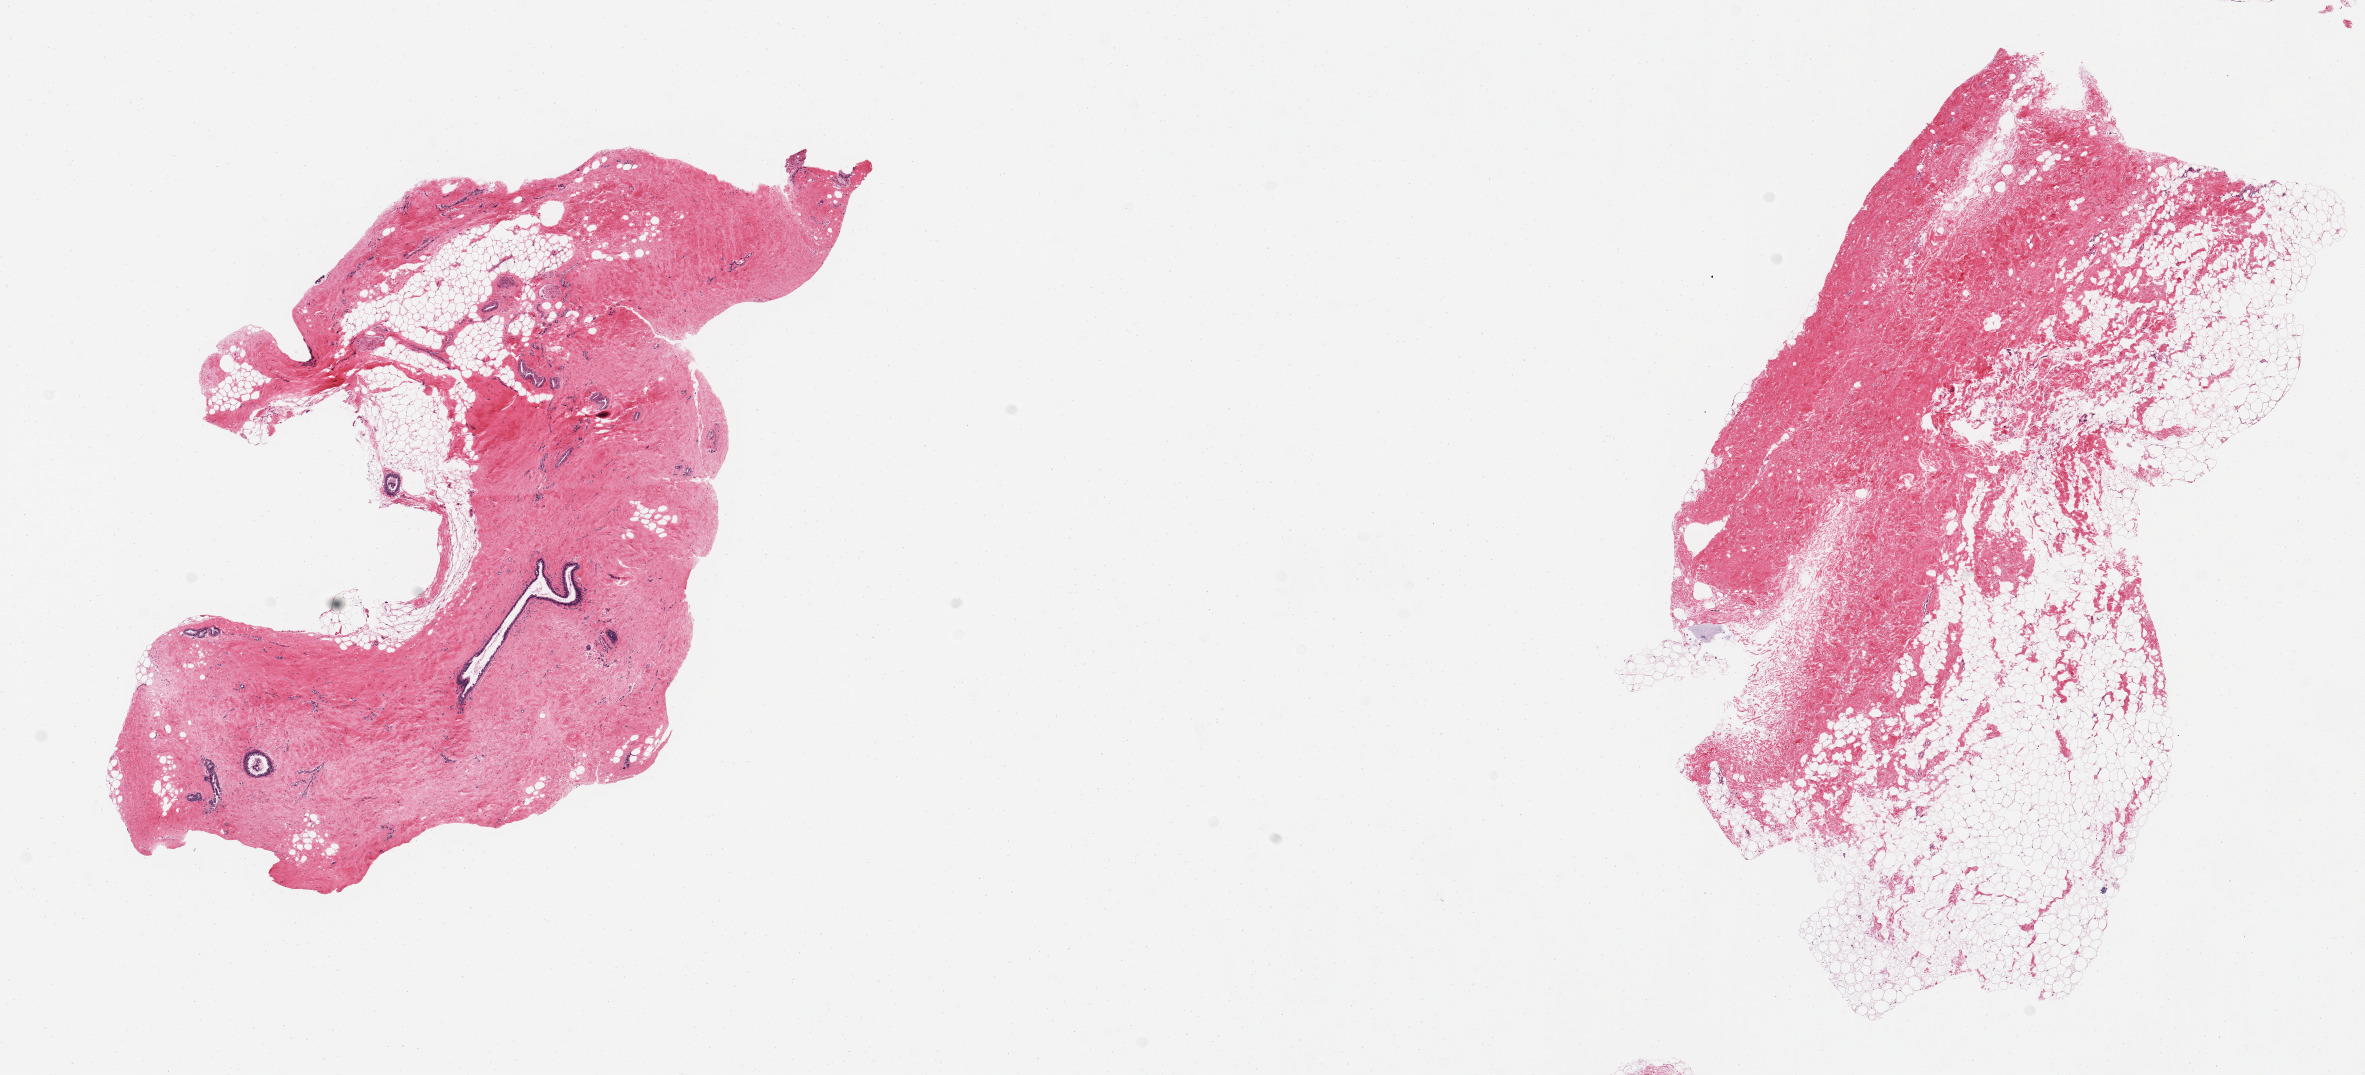
Whole-slide image, haematoxylin and eosin stain, brightfield — low-resolution overview of the scanned area, about 18.7 x 8.5 mm (from a 20x scan); PAXgene-fixed paraffin-embedded (PFPE) section; section of breast (target tissue); donor tissue sample. Male donor.
Pathologist's review note for this sample: 2 pieces; fat and fibrocollagenous stroma, 1 piece includes scattered ducts.